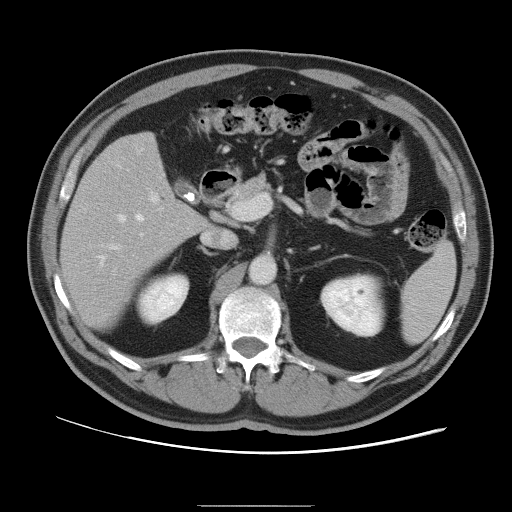
Contrast-enhanced abdominal CT, one axial slice. Position 53 of 105 along the scan axis. 120 kVp. Intravenous contrast given. Soft-tissue window (W 400 / L 40 HU). 512 × 512 image matrix, field of view 399 × 399 mm. Male patient, age 64 years. From the clinical record (not read from this slice): diagnosis: colorectal cancer liver metastases, imaged before liver resection; multiple liver metastases: yes.
Annotated regions visible in this slice (outlined manually by an expert reader):
- hepatic veins: box from (x=99, y=214) to (x=144, y=265) px
- liver: (x=63, y=133)–(x=206, y=330)
- planned liver remnant (the part of the liver to remain after resection): (x=63, y=133)–(x=207, y=329)
- portal vein (with intrahepatic branches): (x=109, y=191)–(x=159, y=250)